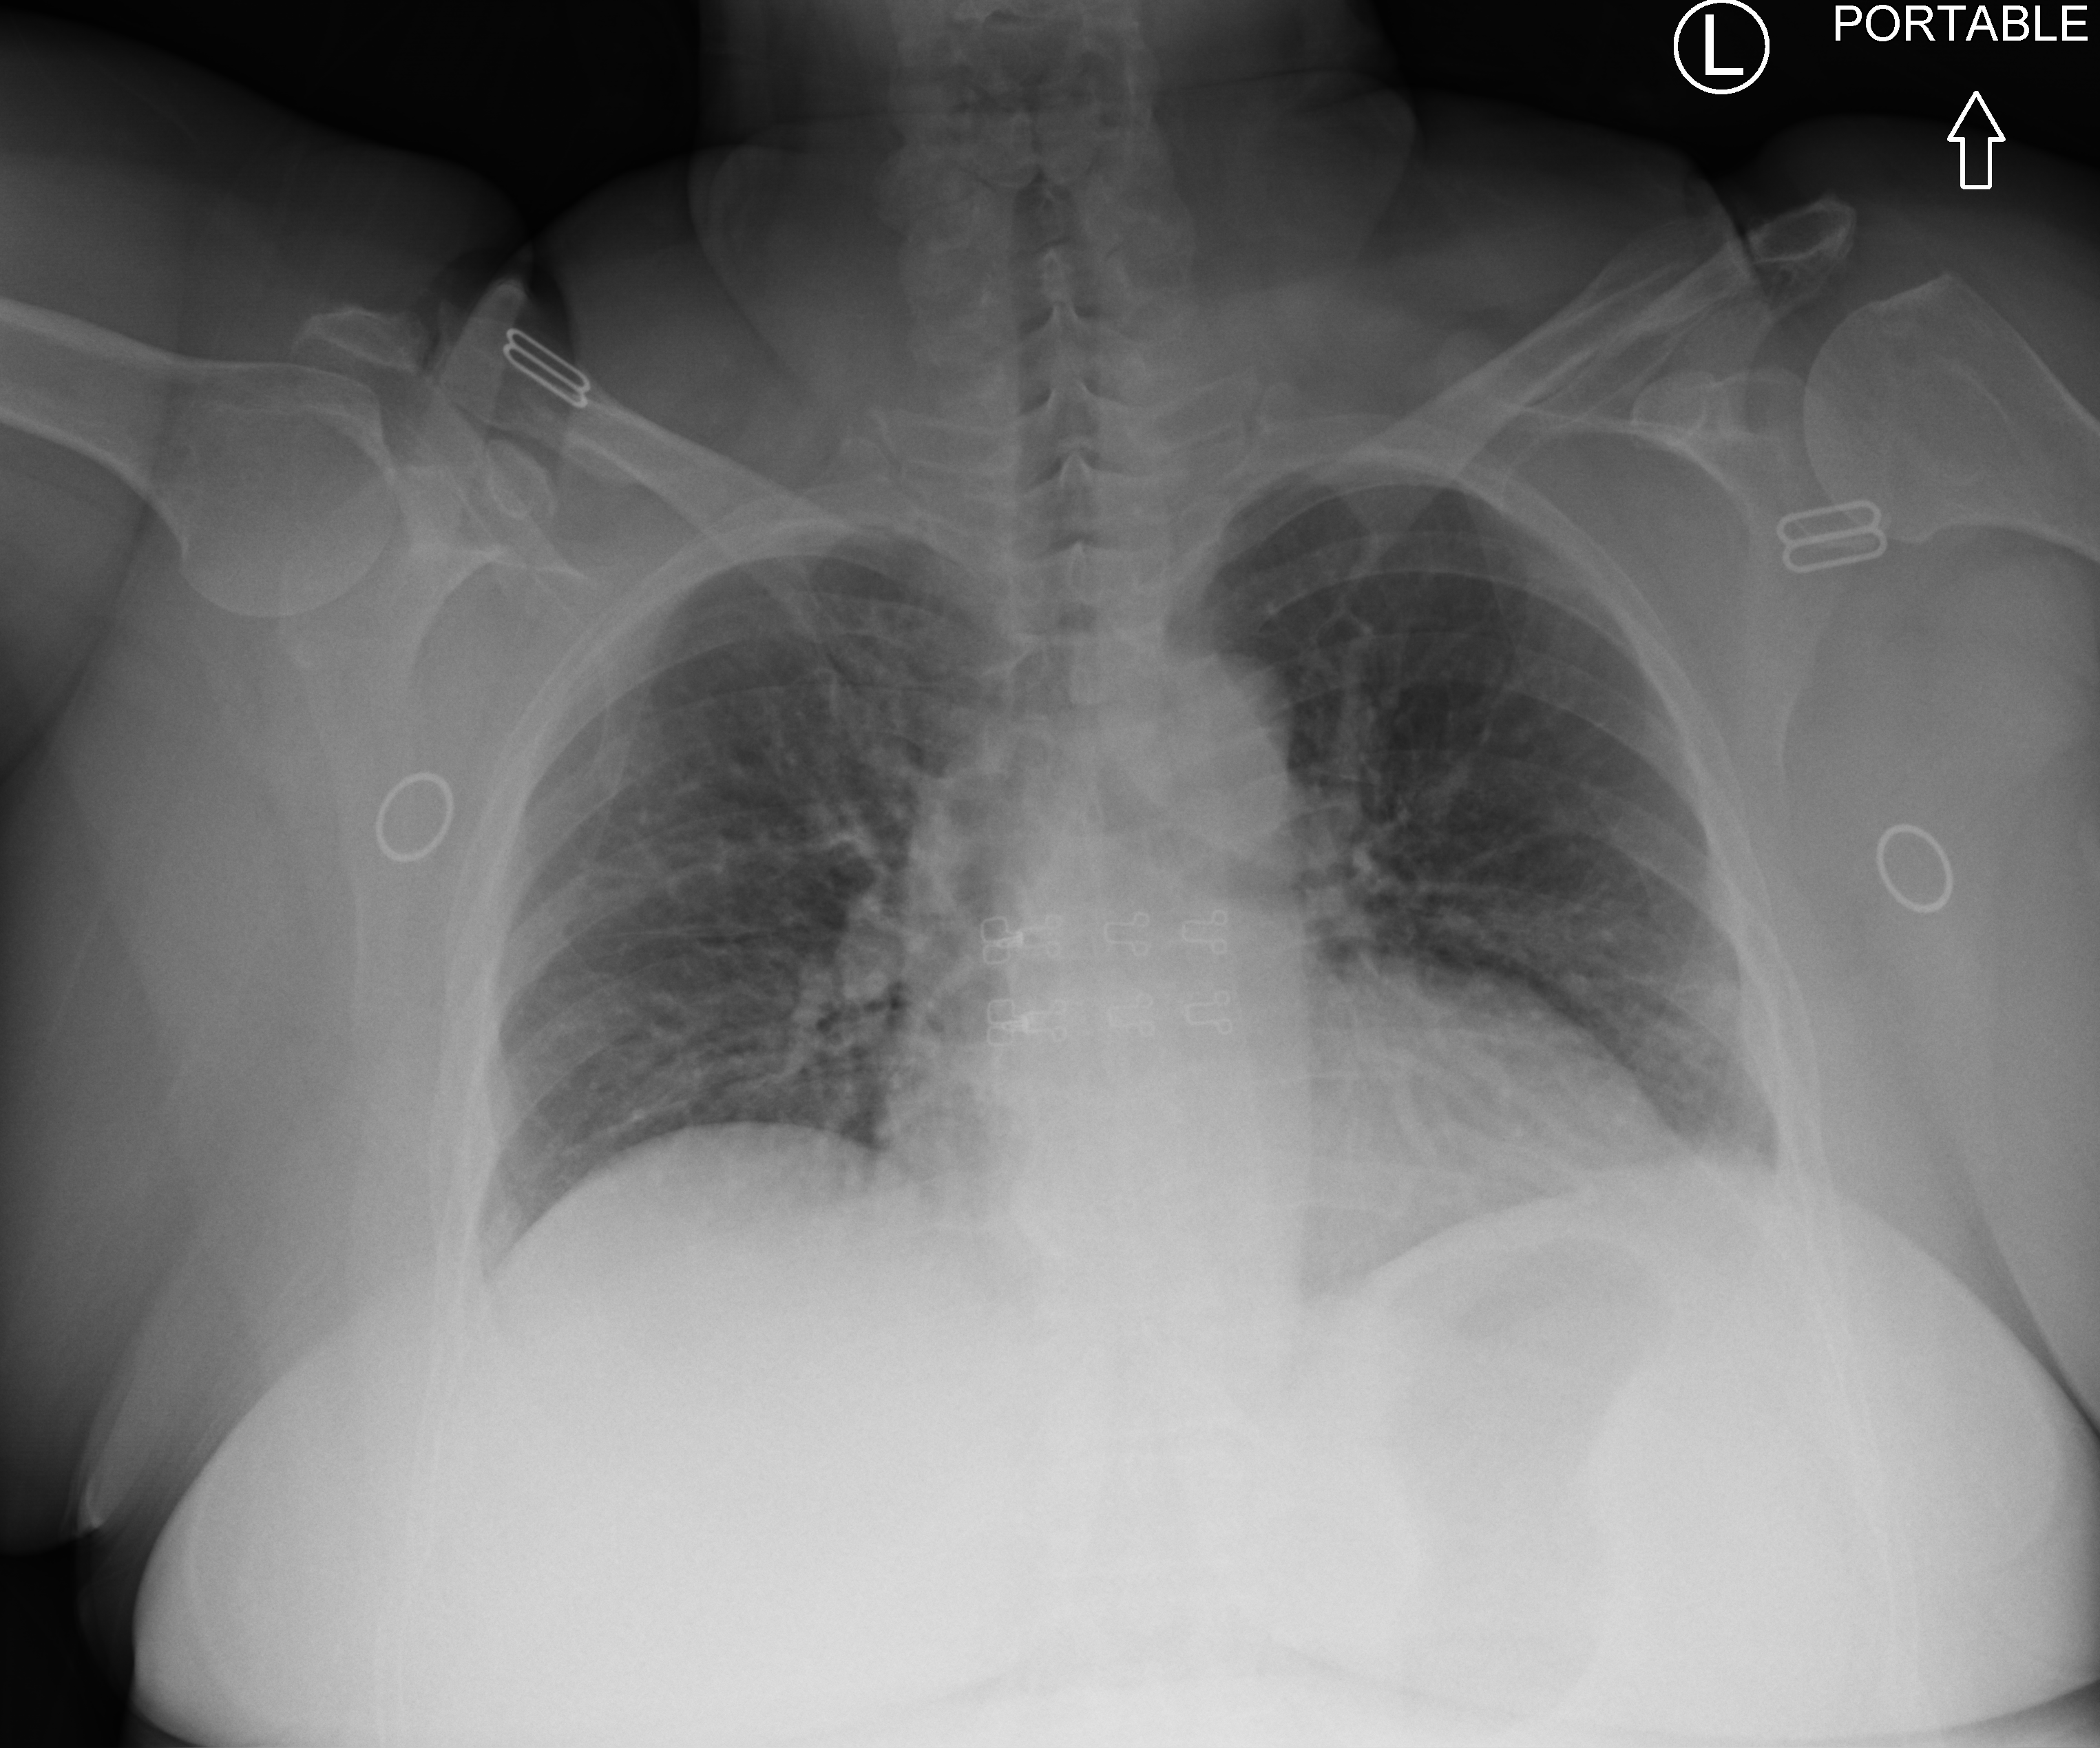
Portable chest radiograph; anteroposterior (AP) projection. Female patient hospitalised with COVID-19, age 60–74 years.
Admission-level facts for this patient (not findings on this image; timing relative to this image not recorded):
- admitted to intensive care during this hospital stay: no
- mechanically ventilated during this hospital stay: no